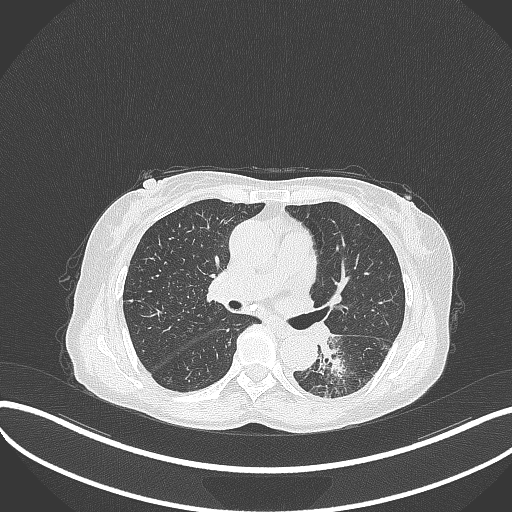
Chest CT, one axial slice; reconstruction kernel B70f; 120 kVp; lung window (W 1500 / L -600 HU); 512 × 512 image matrix. Patient: female, 78 years. Case-level facts recorded for this patient, not image findings: clinical TNM (as recorded): T3 N0 M1.
Outlined on this slice (rectangle marked by the reading radiologist):
- lung tumour (recorded histology: squamous cell carcinoma): bounding box (x1, y1, x2, y2) in pixels: (316, 332, 365, 393)